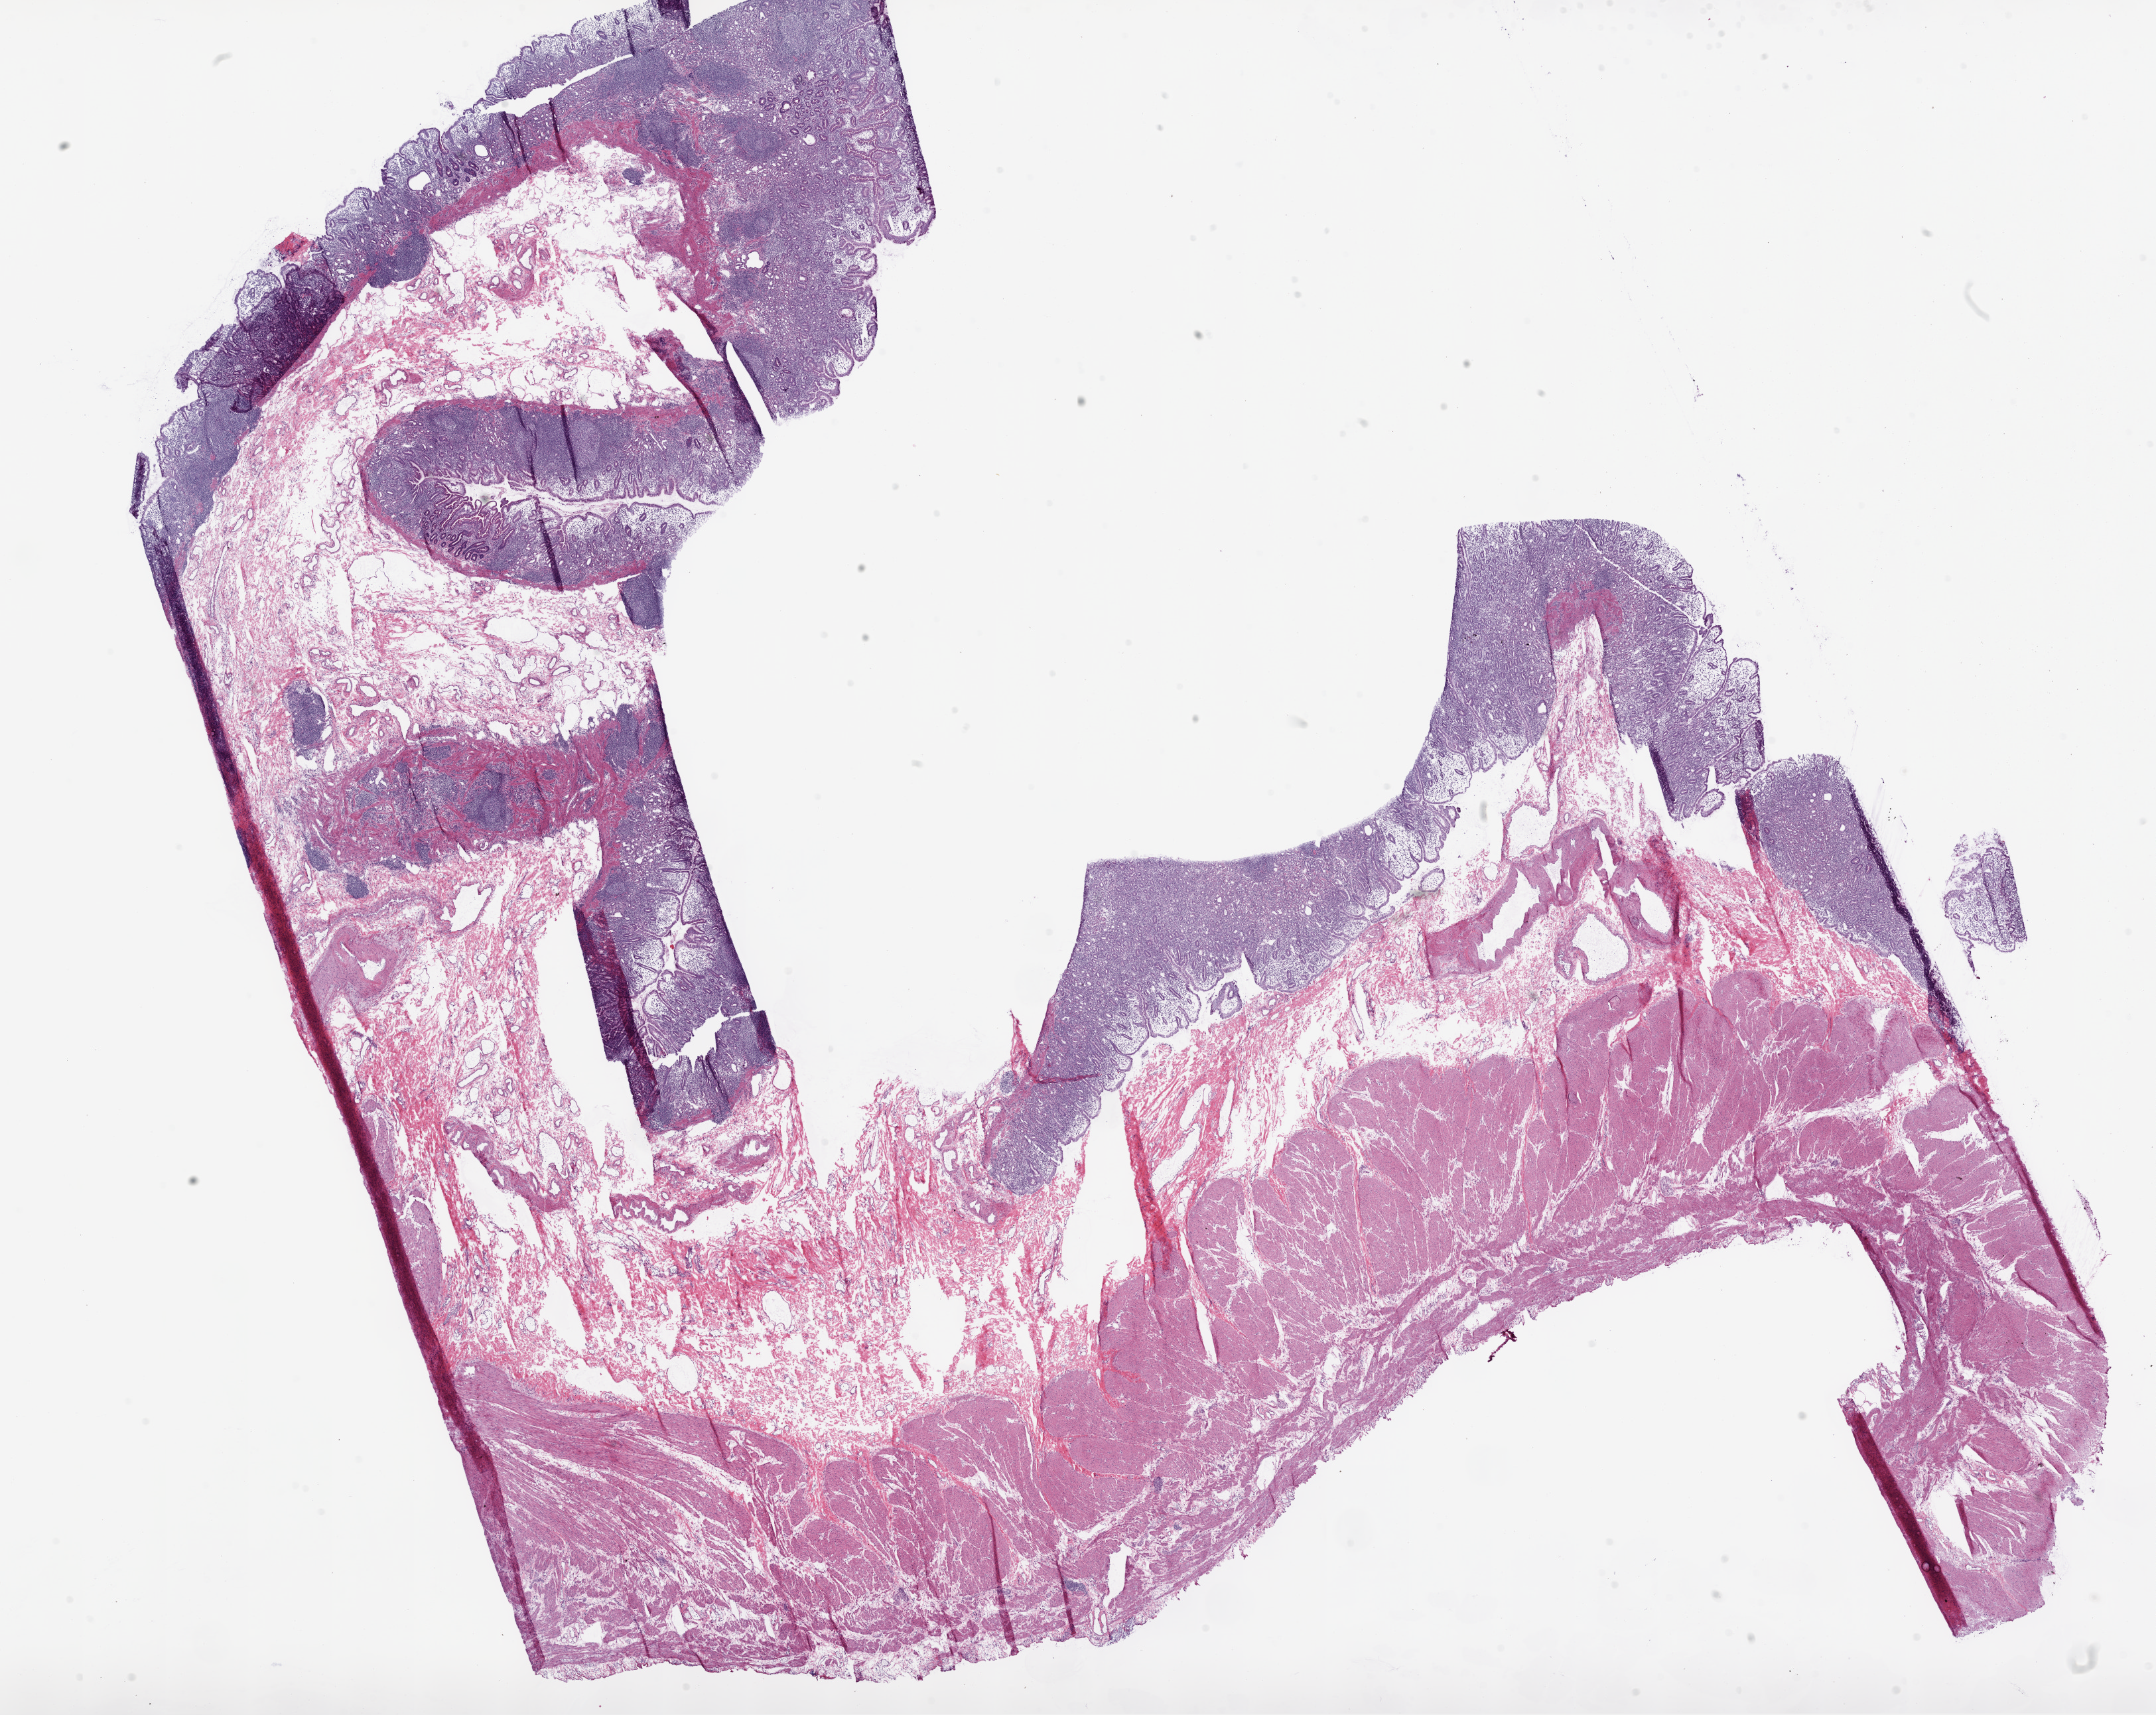
Digitized Hematoxylin and eosin (H&E) stained tissue section (whole slide), shown as a low-resolution overview of the whole scanned area (about 26.1 x 20.7 mm); frozen section from the bottom of the tissue portion; stomach, solid tissue normal (non-tumour tissue) sample. Patient: female, age at initial diagnosis 74 years.
• this section: solid tissue normal sample (biorepository sample class)
• patient diagnosis: Adenocarcinoma, NOS